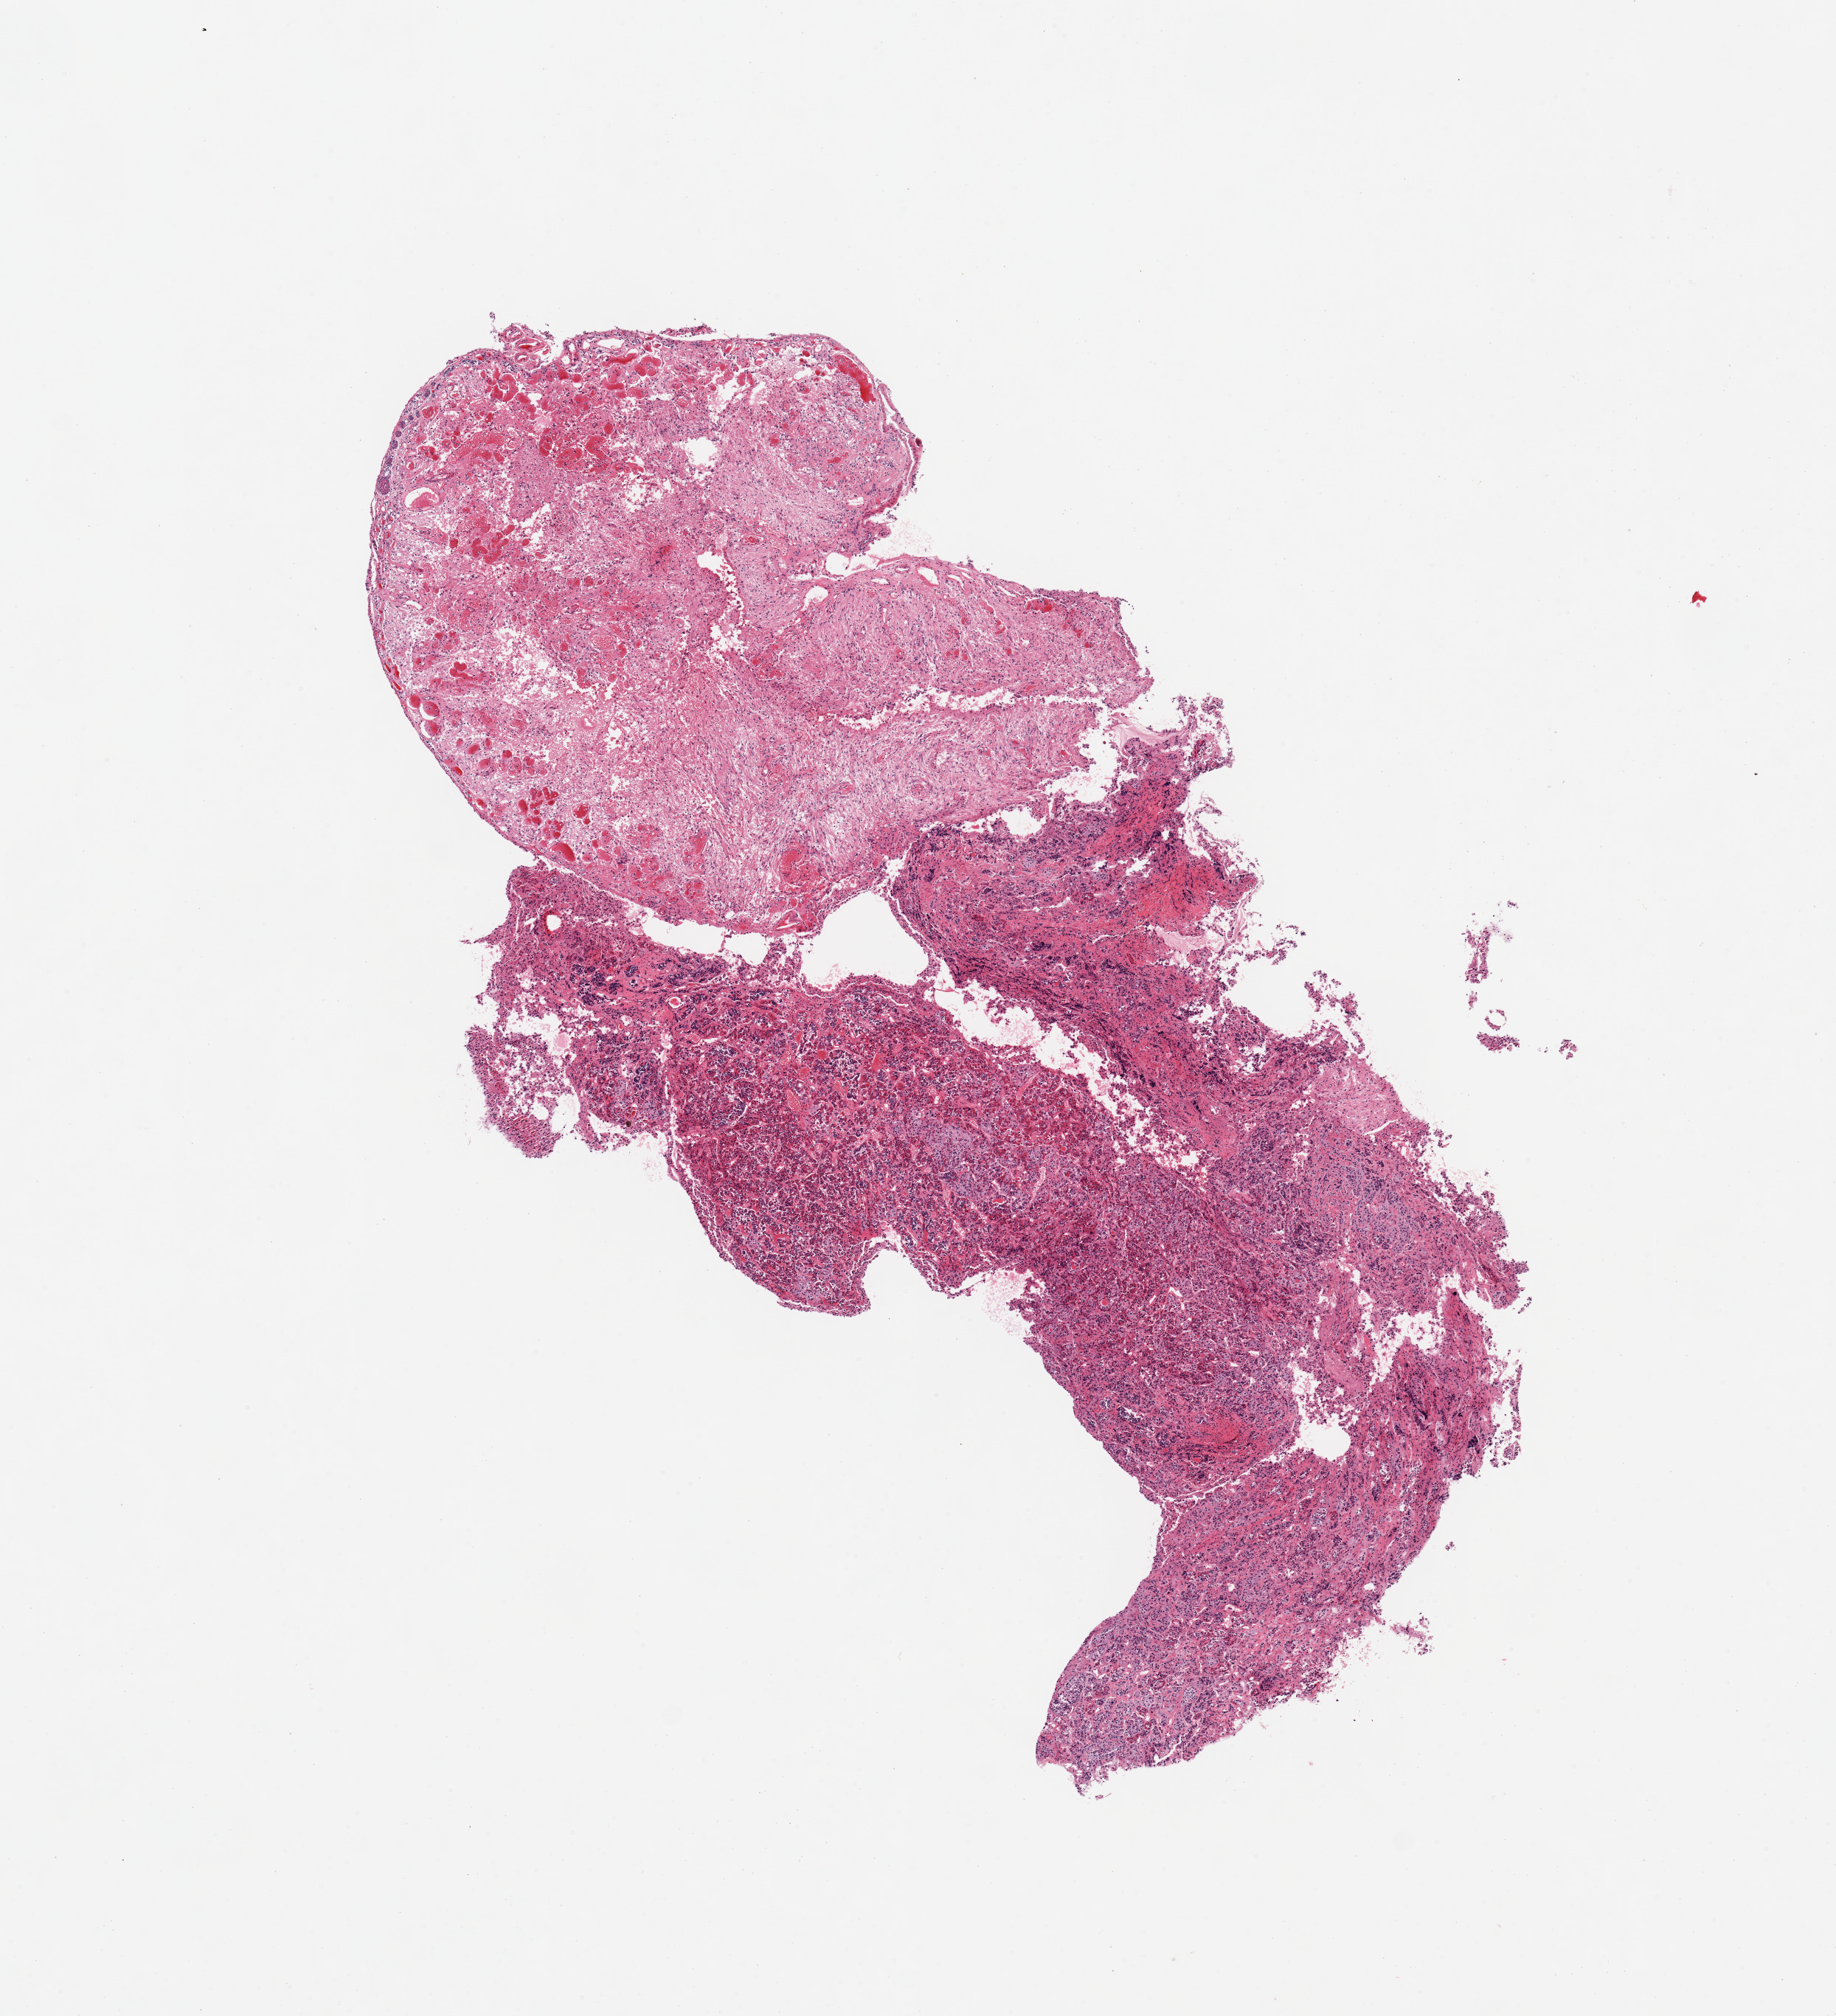
Whole-slide image, hematoxylin and eosin (H&E) stain, low-resolution overview of the scanned area, about 9.8 x 10.8 mm (from a 20x scan). PAXgene-fixed paraffin-embedded (PFPE) section. Sampled site (target tissue): pituitary. Donor tissue sample. Donor: female.
Pathologist's review note for this sample: 1 piece, ~50% neurohypophysis; rest is adenohypophysis.